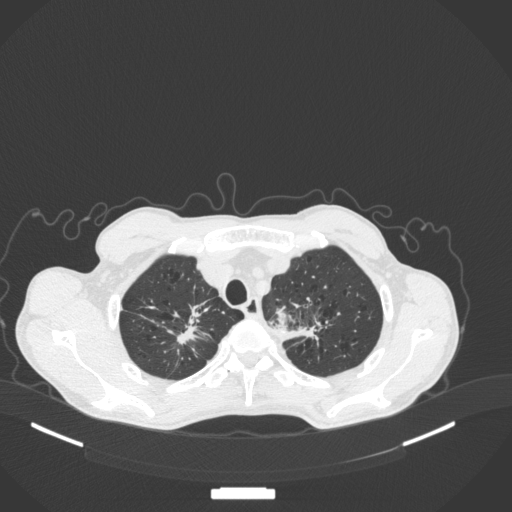
Chest CT, one axial slice. Position 366 of 394 along the scan axis. Reconstruction kernel B31f. Lung window (W 1500 / L -600 HU). 512 × 512 image matrix, field of view 400 × 400 mm. Male patient, age 65 years. From the clinical record (not read from this slice): clinical TNM (as recorded): T2b N0 M0.
Structures marked on this image (bounding box drawn by a radiologist):
- lung tumour (recorded histology: adenocarcinoma): bounding box (x1, y1, x2, y2) in pixels: (274, 303, 293, 333)